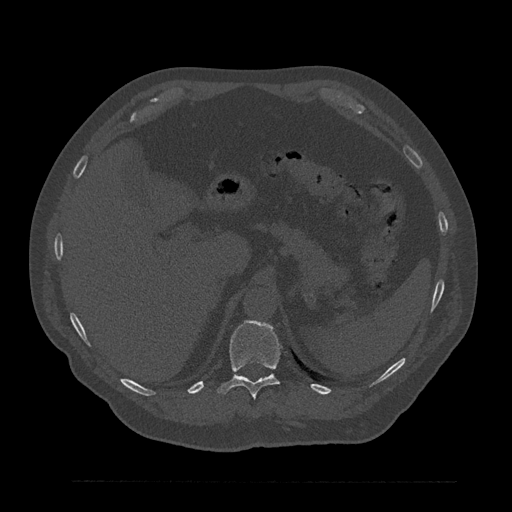
CT including the spine, one axial slice; slice 289 of 797 in the series (ordered by position); reconstruction kernel Br40s/3; bone window (W 1800 / L 400 HU); 0.5 mm slice thickness; 512 × 512 image matrix, field of view 430 × 430 mm. Male patient, age 61 years. From the clinical record (not read from this slice): primary cancer: prostate.
Annotated regions visible in this slice (semi-automatically segmented with operator editing):
- T11 vertebra: bounding box [x1, y1, x2, y2] px = [217, 320, 281, 399]